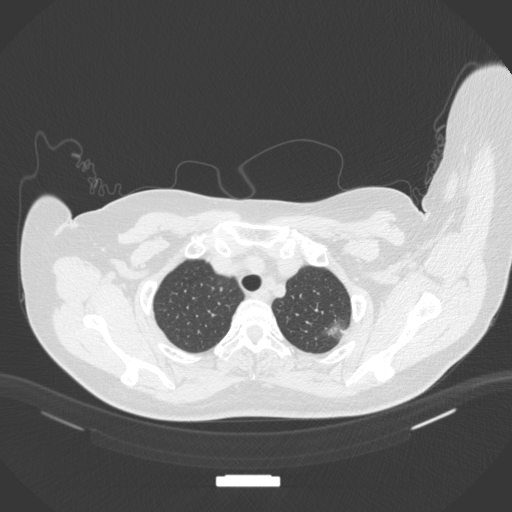
Chest CT, one axial slice; position 318 of 386 along the scan axis; reconstruction kernel B31f; 120 kVp; lung window (W 1500 / L -600 HU); 1 mm slice thickness; 512 × 512 image matrix, field of view 400 × 400 mm. Patient: female, 58 years. Case-level facts recorded for this patient, not image findings: clinical TNM (as recorded): T1c N0 M0.
Annotated regions visible in this slice (bounding box drawn by a radiologist):
- lung tumour (recorded histology: adenocarcinoma): bounding box <323,317,353,344> (left, top, right, bottom; pixels)